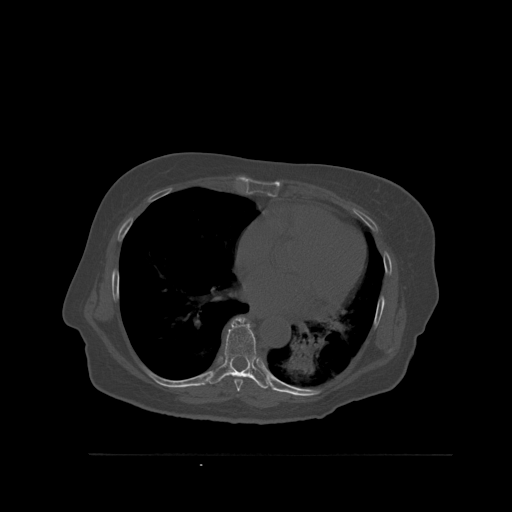
CT including the spine, one axial slice. Slice 354 of 527 in the series (ordered by position). Bone window (W 1800 / L 400 HU). 1.5 mm slice thickness. 512 × 512 image matrix, field of view 470 × 470 mm. Female patient, age 73 years. From the clinical record (not read from this slice): primary cancer: breast; vertebrae with lytic lesions (as recorded): L2.
Annotated regions visible in this slice (semi-automatic segmentation, software-assisted and operator-edited):
- T7 vertebra: bounding box [x1, y1, x2, y2] px = [234, 377, 257, 392]
- T8 vertebra: [209, 317, 269, 389]